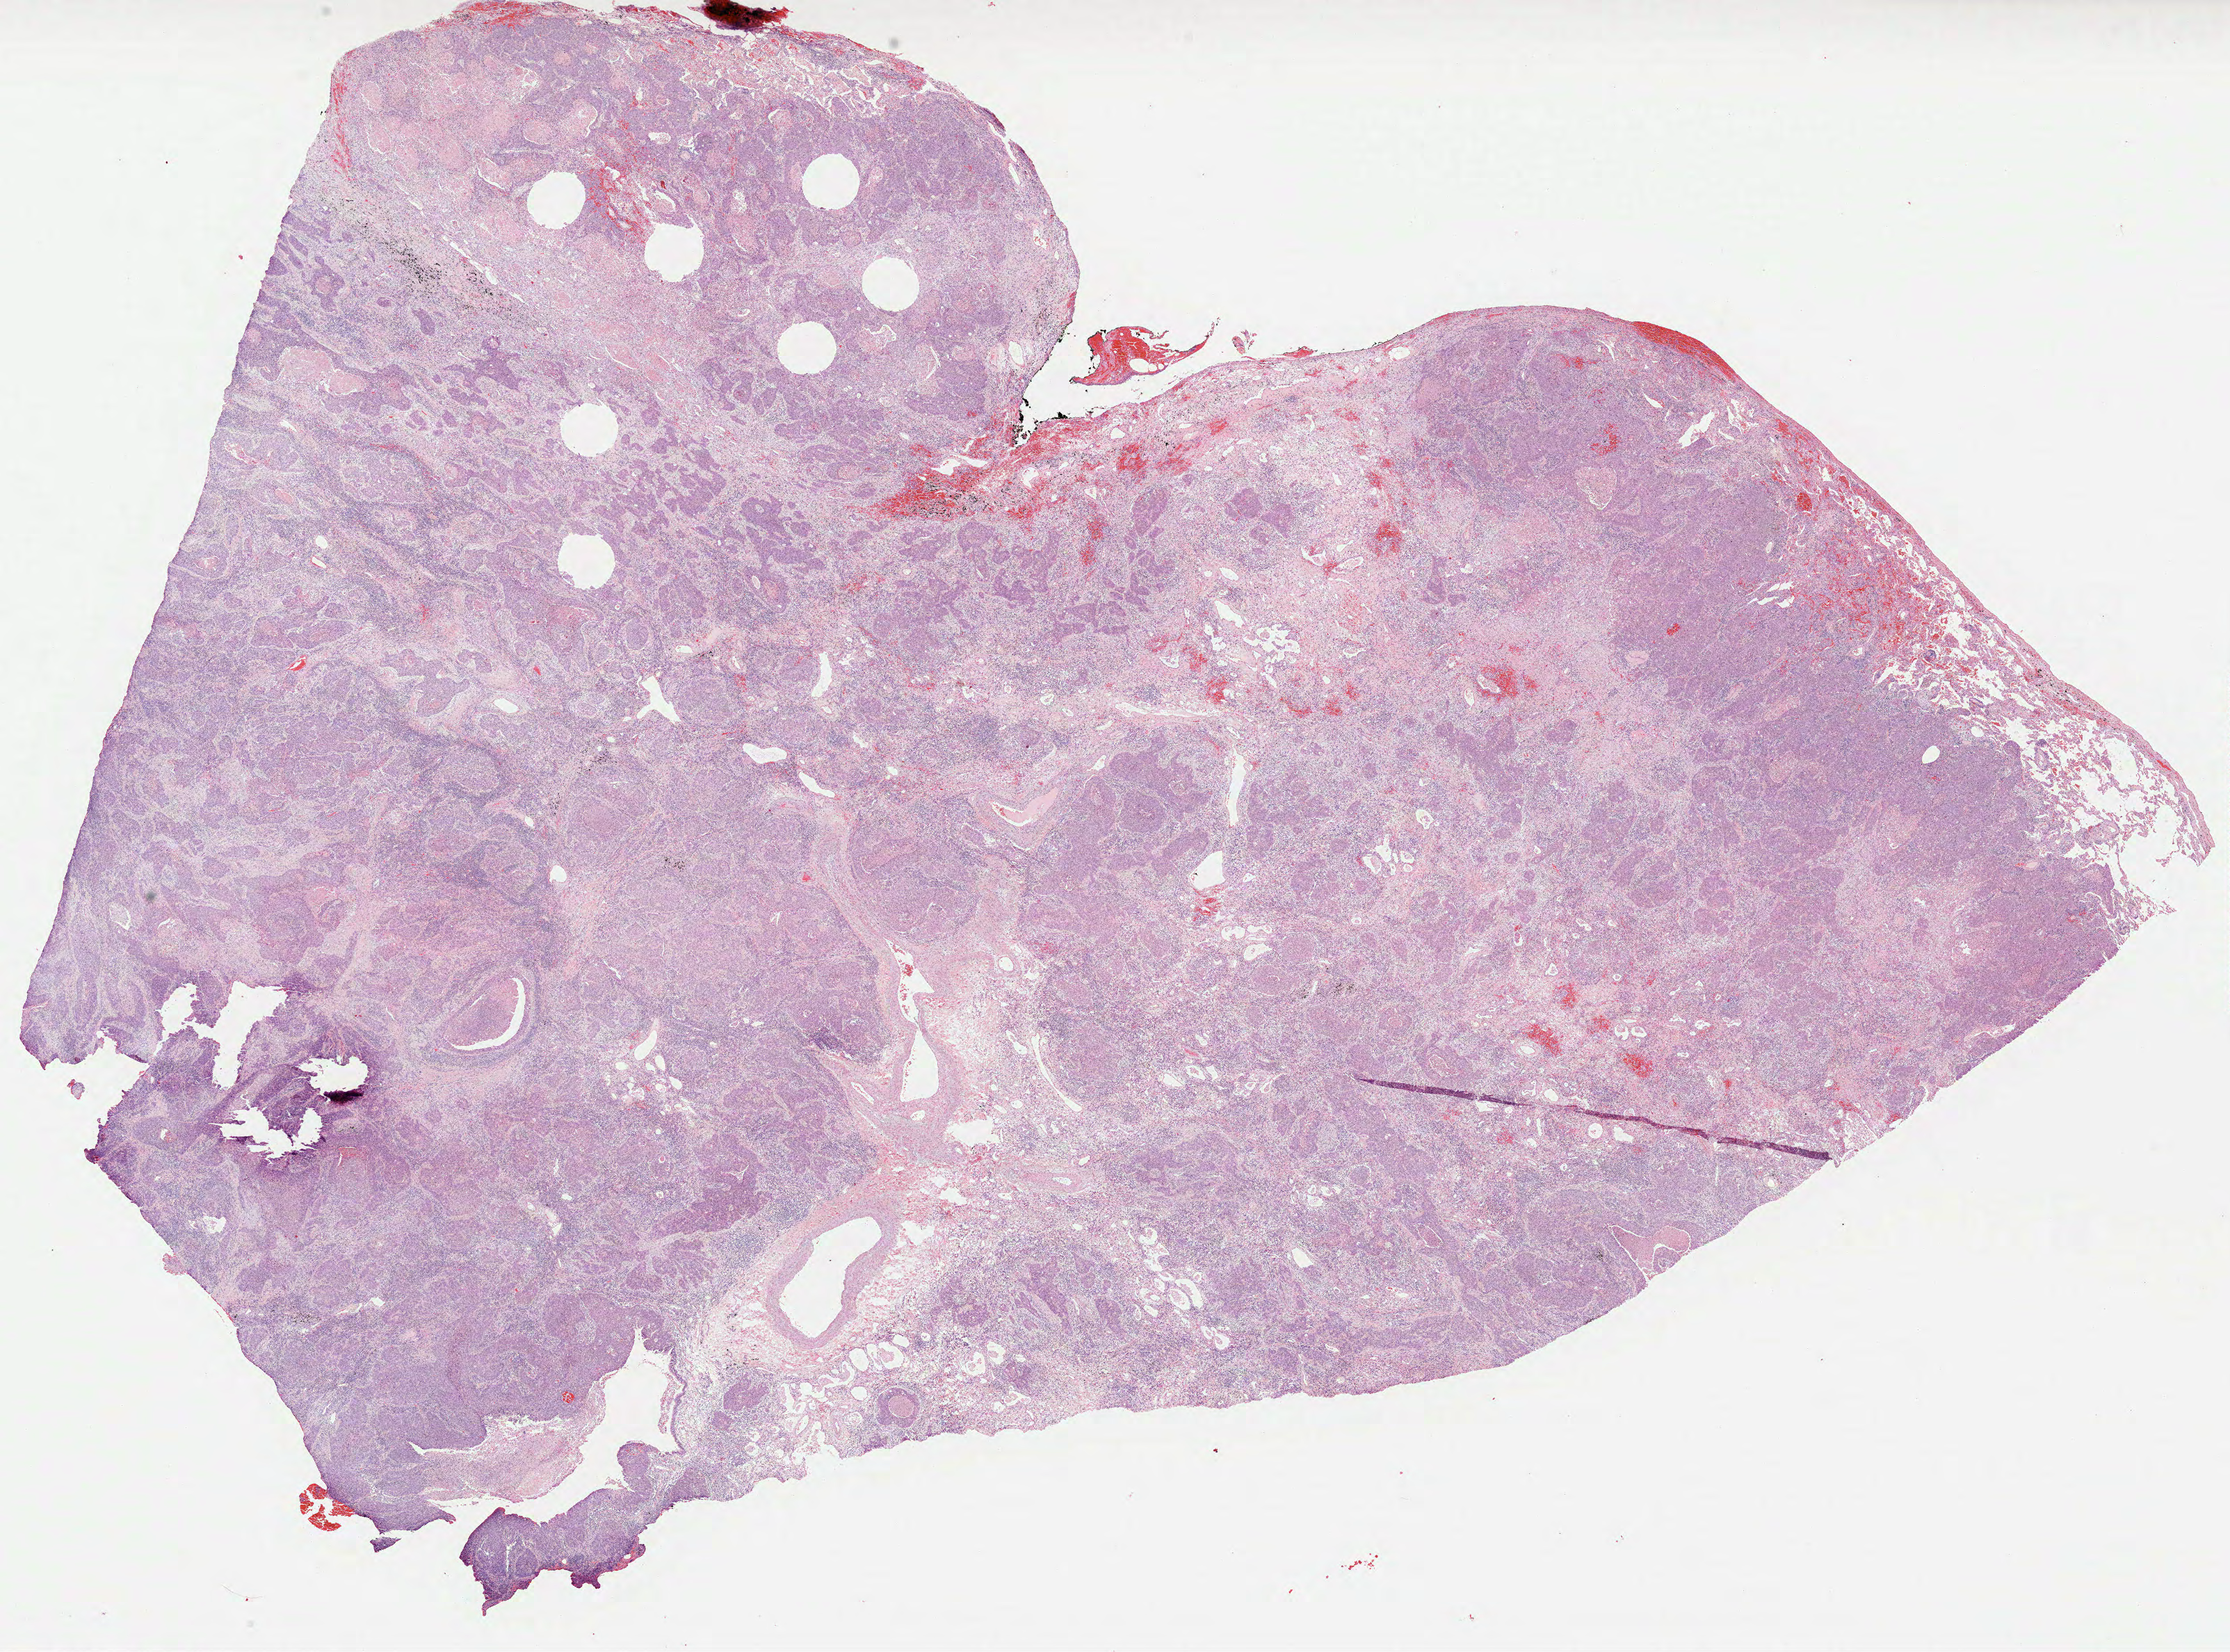
H&E whole-slide image — shown as a low-resolution overview of the whole scanned area (about 25.9 x 19.2 mm, from a 40x scan); FFPE section; primary tumour sample from the lung. Male, age 74 years at initial diagnosis.
AJCC pathologic stage: IB. Laterality: left. Histologic diagnosis: Squamous cell carcinoma, NOS (upper lobe, lung).